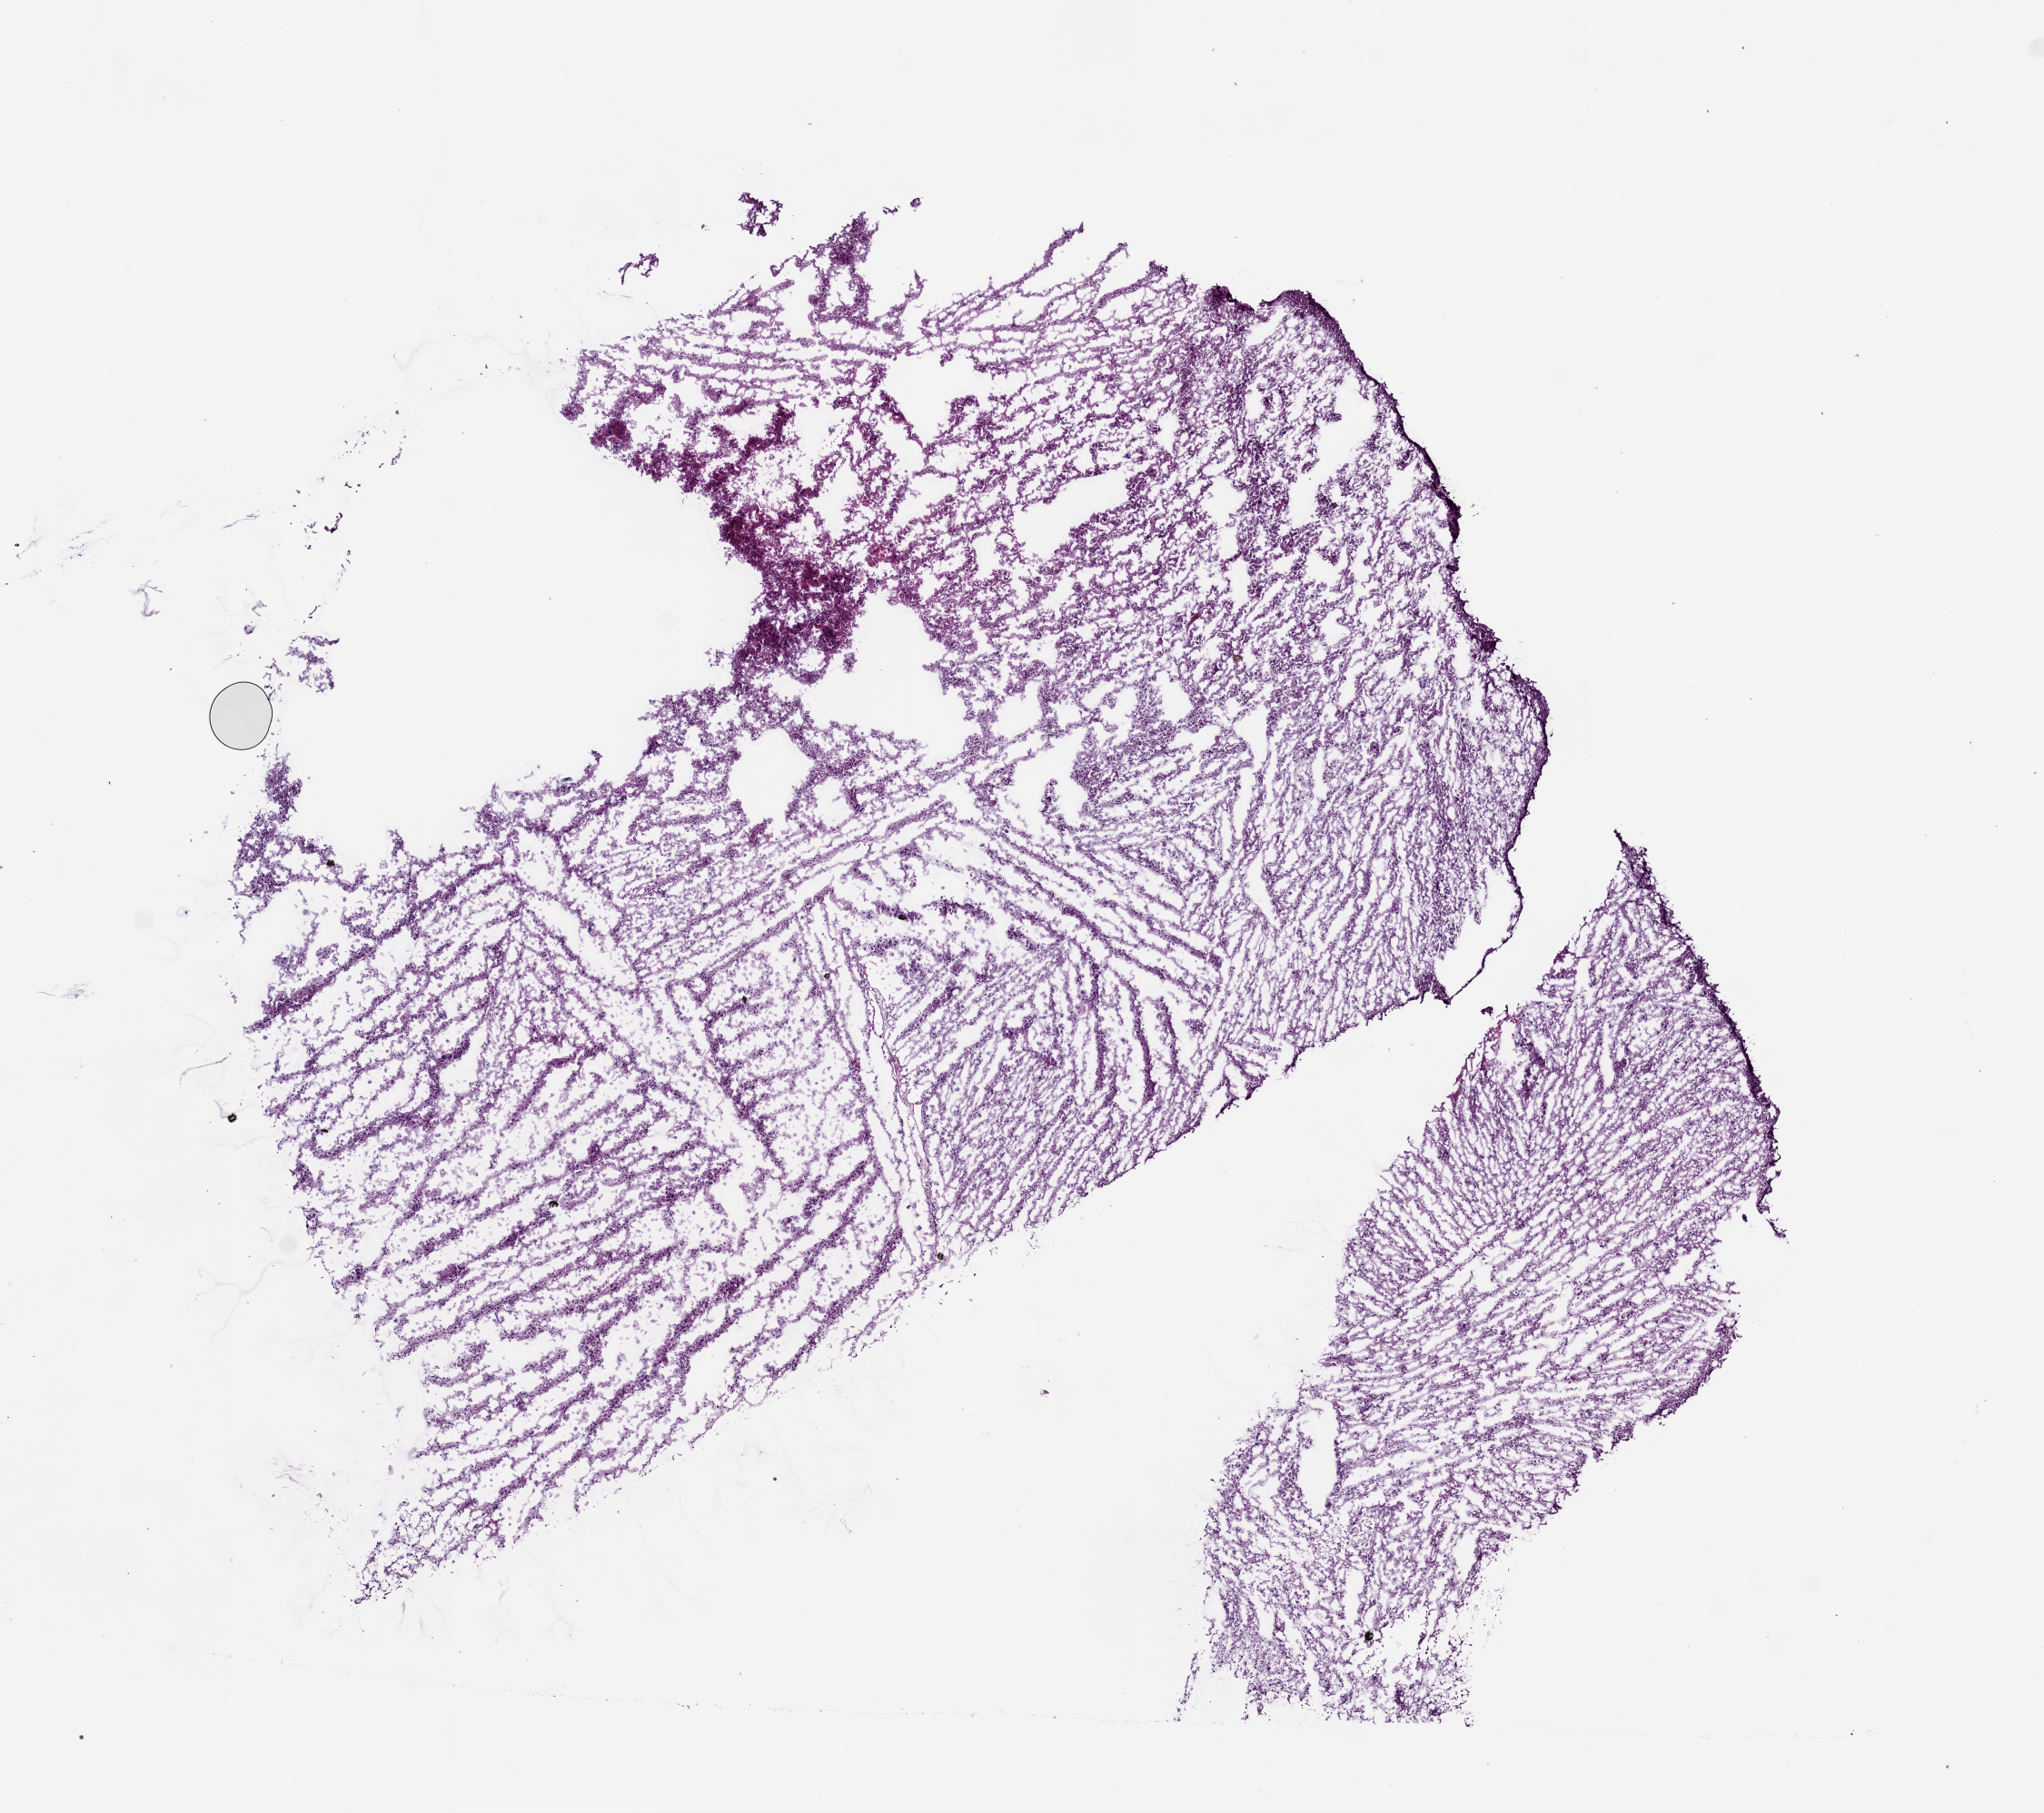
Hematoxylin and eosin (H&E) stained whole-slide image — whole scanned area (about 9.0 x 8.0 mm, acquisition: 20x scan) shown as a low-resolution overview; frozen section; brain, primary tumour sample. Male patient; age at initial diagnosis 37 years. Histologic grade: G3 (poorly differentiated). Pathologist review of this section (percent, as recorded): tumour cells 100%, tumour nuclei 80%, normal cells 0%, stromal cells 0%, necrosis 0%.
Diagnosis: Astrocytoma, anaplastic. Laterality: left.